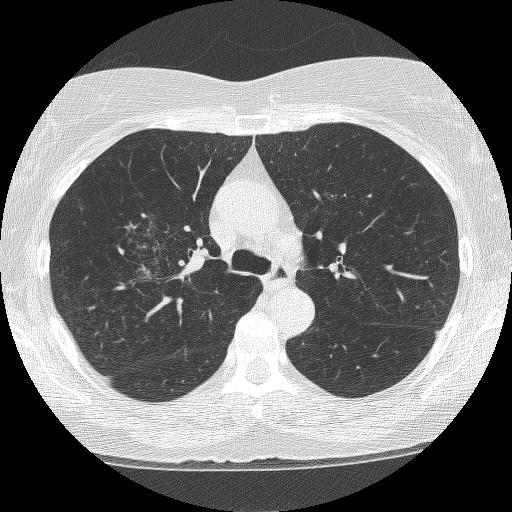
Axial slice from a low-dose chest CT screening exam, second annual screen, lung window (W 1500 / L -600 HU), 1.25 mm slice thickness, lung (sharp) reconstruction kernel (BONE), slice 166 of 249 in the series. Female, age 64 years at enrolment. Former smoker at enrolment.
- Expert reader's lesion annotation, box from (x=114, y=204) to (x=210, y=294) px.
- The screening reader recorded 4 non-calcified nodules or masses ≥4 mm on this exam (right upper lobe, right upper lobe, right upper lobe, left upper lobe); which of them this box marks is not recorded.
- Later outcome: lung cancer diagnosed 381 days after this screen — adenocarcinoma, NOS, right upper lobe, right middle lobe, right hilum, stage IV (AJCC 6th edition), 85 mm at pathology.